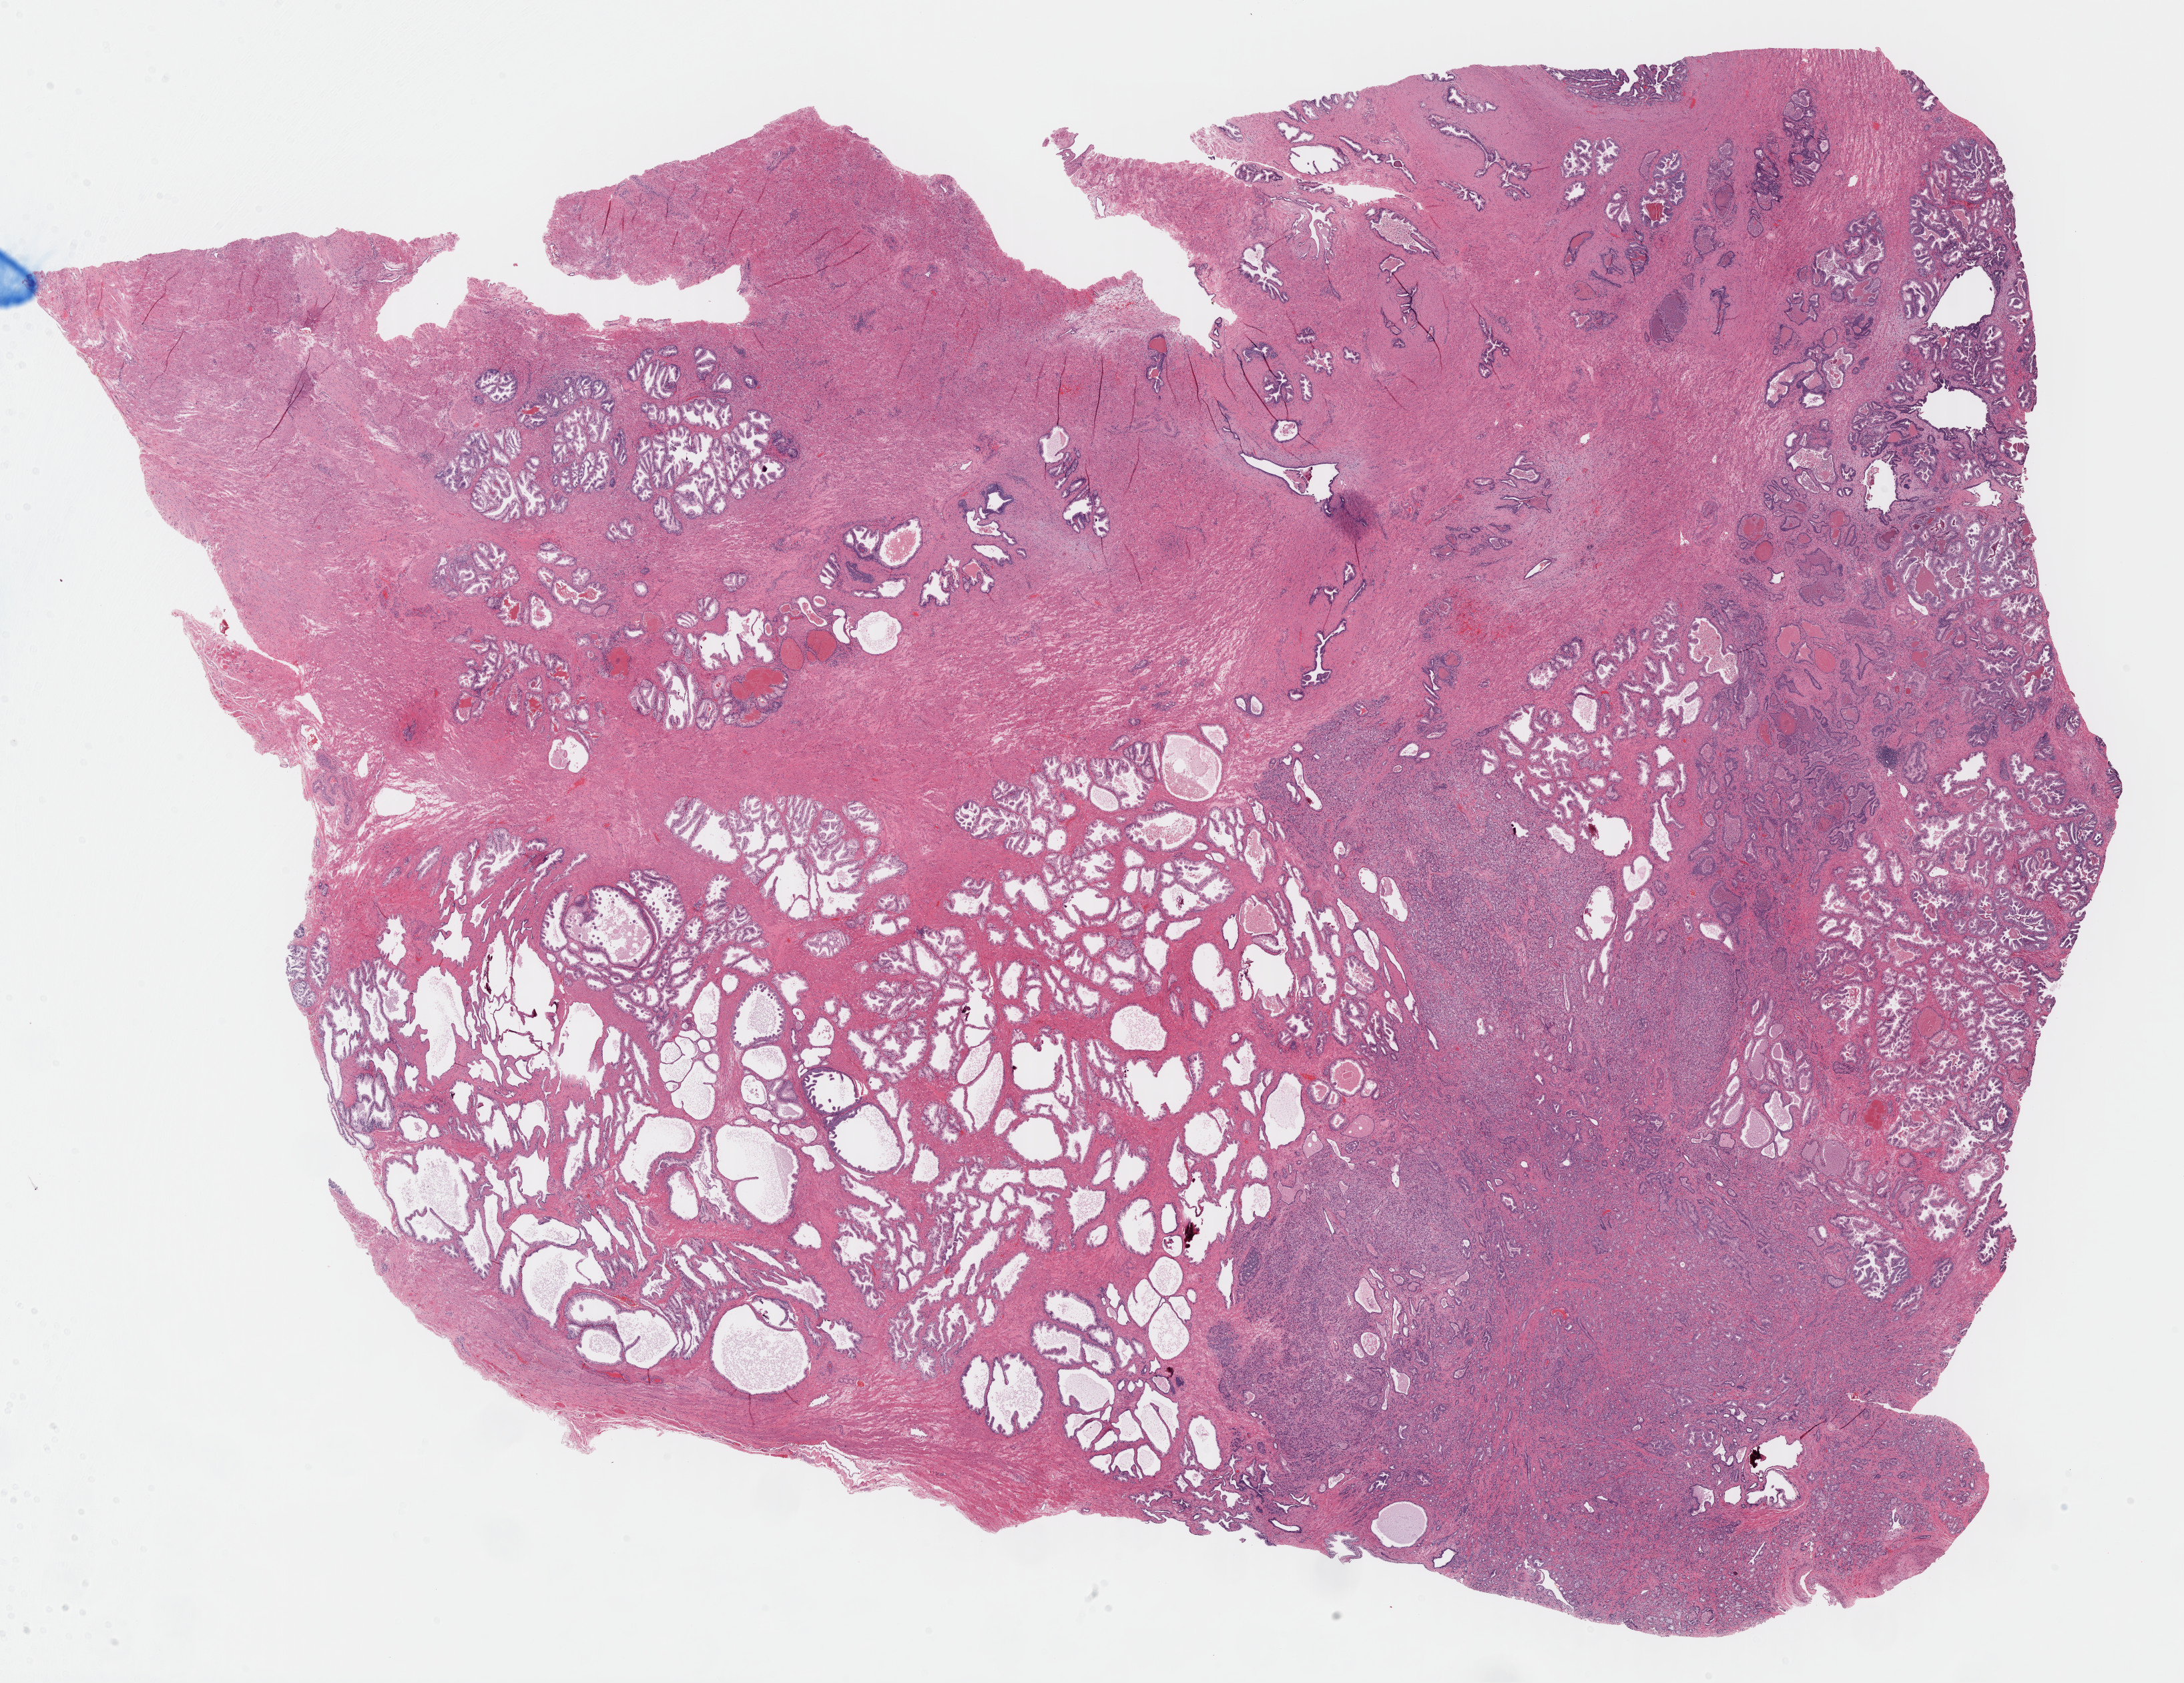
Digitized H&E-stained tissue section (whole slide), low-resolution overview of the scanned area, about 25.7 x 19.8 mm (slide scanned at 40x). Formalin-fixed paraffin-embedded (FFPE) diagnostic section. Prostate, primary tumour sample. Male patient; age at initial diagnosis 66 years. Gleason score: 8 (4+4).
Lymph nodes positive (case pathology): 0 of 10 examined. Diagnosis: Adenocarcinoma, NOS (prostate gland).